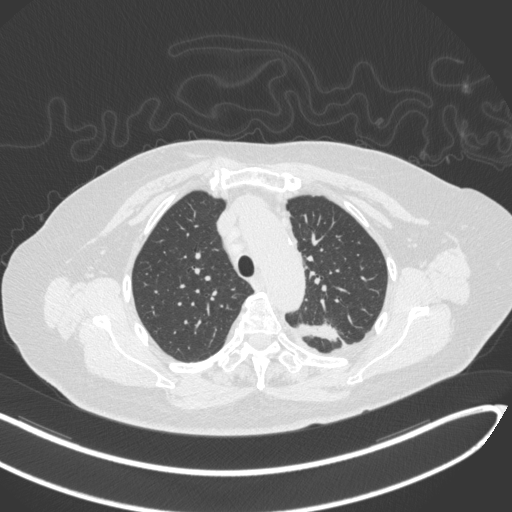
Chest CT, one axial slice. Position 239 of 270 along the scan axis. Reconstruction kernel B31f. 120 kVp. Lung window (W 1500 / L -600 HU). 1 mm slice thickness. 512 × 512 image matrix, field of view 400 × 400 mm. Patient: female, 76 years. From the clinical record (not read from this slice): clinical TNM (as recorded): T1c N0 M0.
Outlined on this slice (rectangle marked by the reading radiologist):
- lung tumour (recorded histology: adenocarcinoma): bounding box <296,319,339,348> (left, top, right, bottom; pixels)